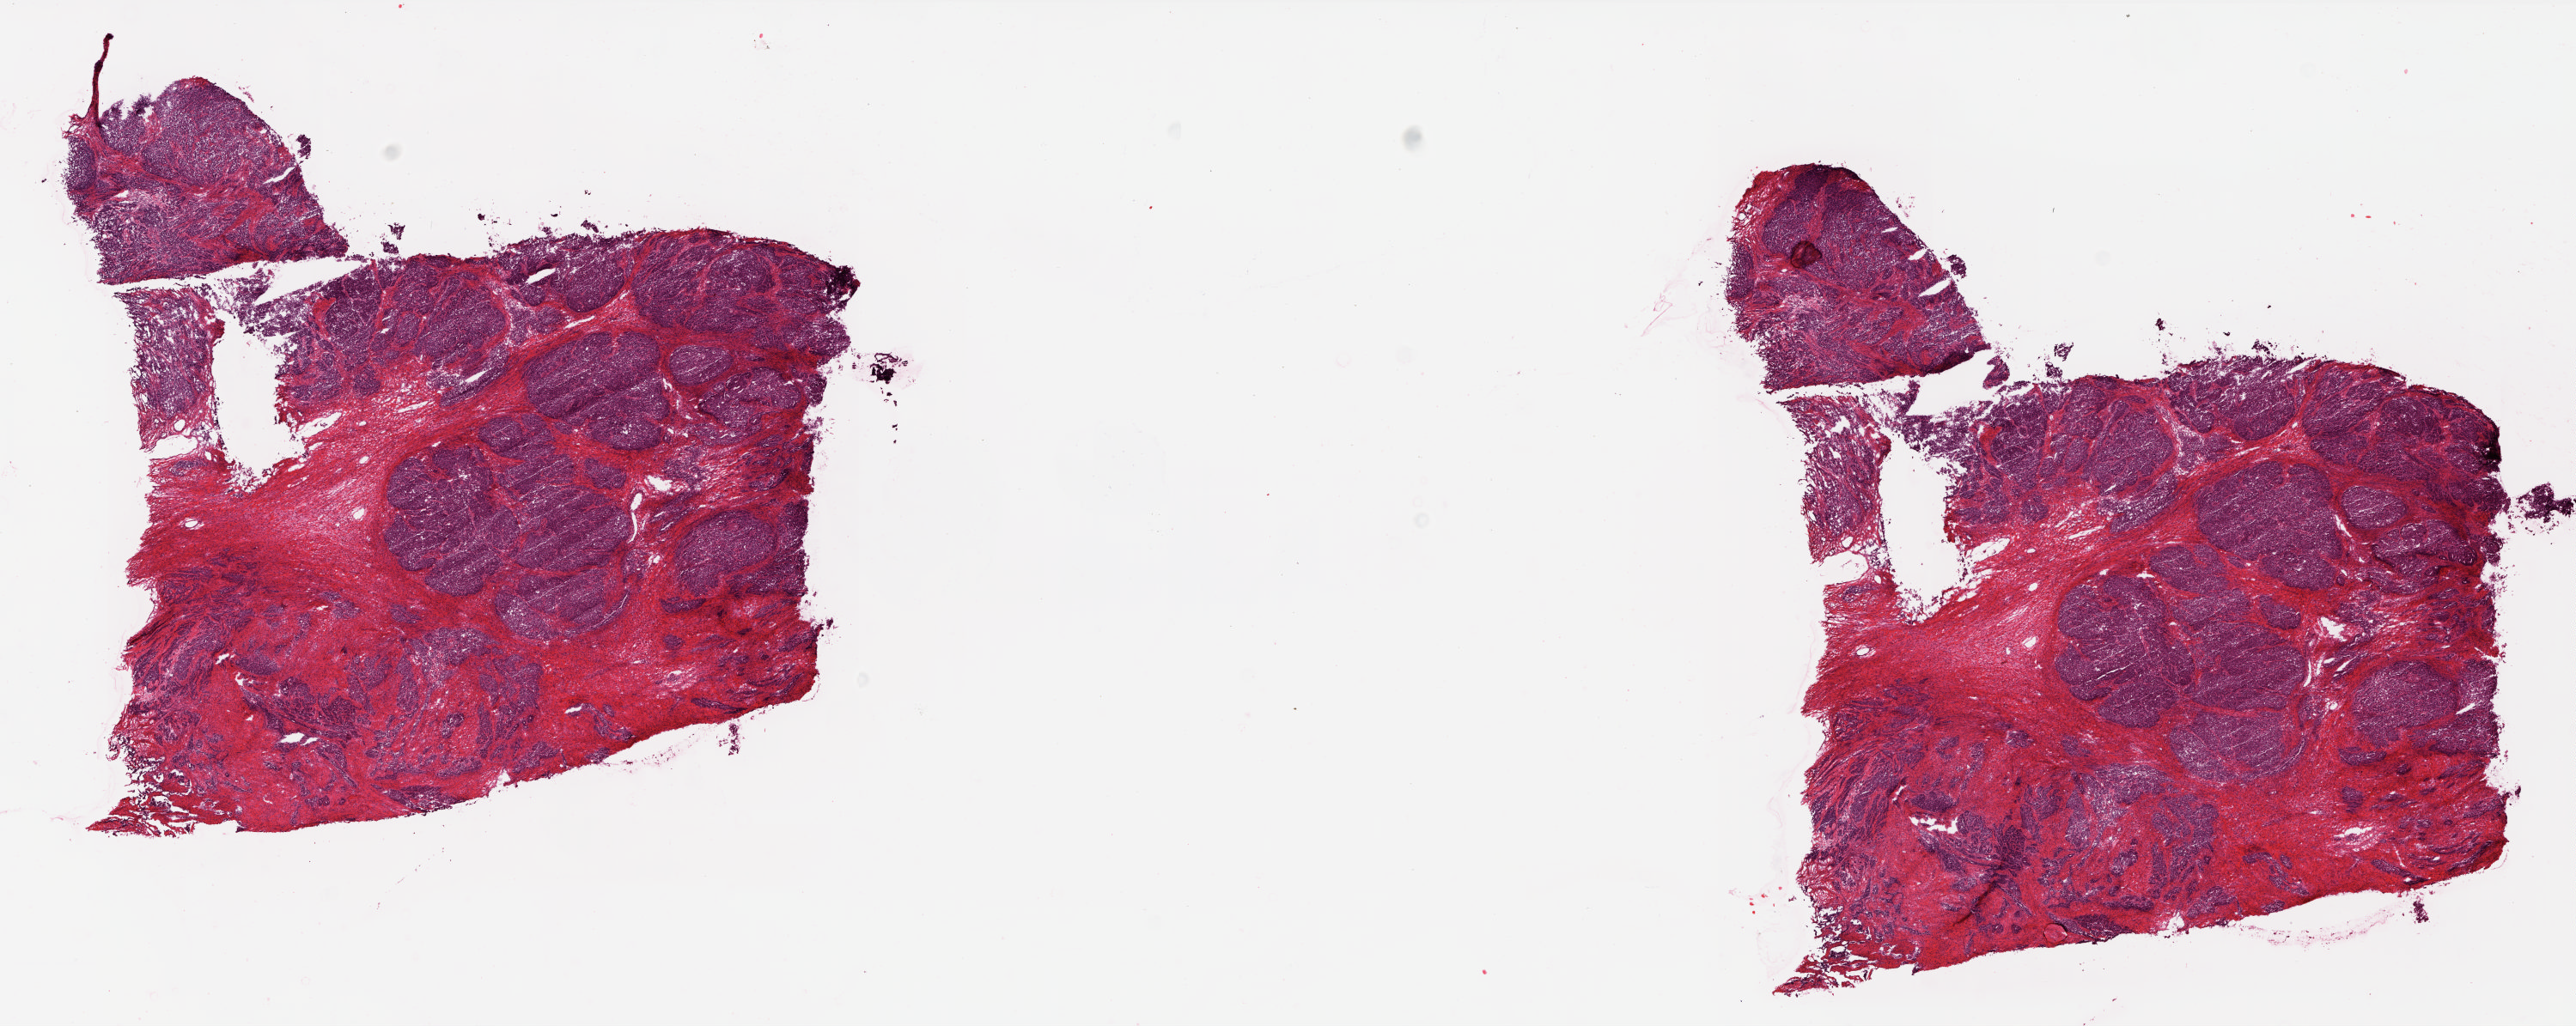
Digitized H&E-stained tissue section (whole slide) — shown as a low-resolution overview of the whole scanned area (about 24.0 x 9.5 mm, from a 20x scan). Frozen section from the top of the tissue portion. Primary tumour sample from the ovary. Patient: female, age at initial diagnosis 57 years. Histologic grade: G3 (poorly differentiated). Slide review estimates, as recorded: tumour cells 69%, tumour nuclei 80%, normal cells 0%, stromal cells 30%, necrosis 1%.
- laterality: bilateral
- histologic diagnosis: Serous cystadenocarcinoma, NOS
- FIGO stage: IIIB